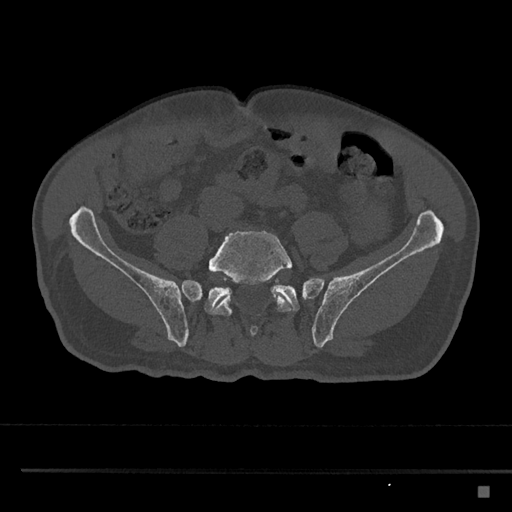
CT including the spine, one axial slice. Slice 566 of 797 in the series (ordered by position). 120 kVp. Bone window (W 1800 / L 400 HU). 0.5 mm slice thickness. 512 × 512 image matrix, field of view 391 × 391 mm. Male patient, age 59 years. From the clinical record (not read from this slice): primary cancer: prostate.
Structures marked on this image (semi-automatically segmented with operator editing):
- L5 vertebra: box from (x=208, y=230) to (x=292, y=336) px